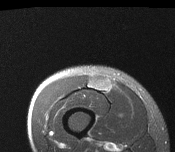
MRI of an extremity soft-tissue mass, one axial slice. Slice 33 of 116 in the series (ordered by position). T2-weighted fat-saturated. MR volume resampled by the dataset authors to the PET/CT grid (not the native acquisition matrix). 3.27 mm slice thickness. 175 × 152 image matrix. Male patient. Case-level facts recorded for this patient, not image findings: histological type: pleiomorphic leiomyosarcoma; grade: intermediate; site of the primary tumour: right thigh.
Outlined on this slice (expert contour drawn on MRI and transferred to this co-registered scan by the dataset authors):
- gross tumour volume including surrounding oedema: bounding box <88,77,112,93> (left, top, right, bottom; pixels)